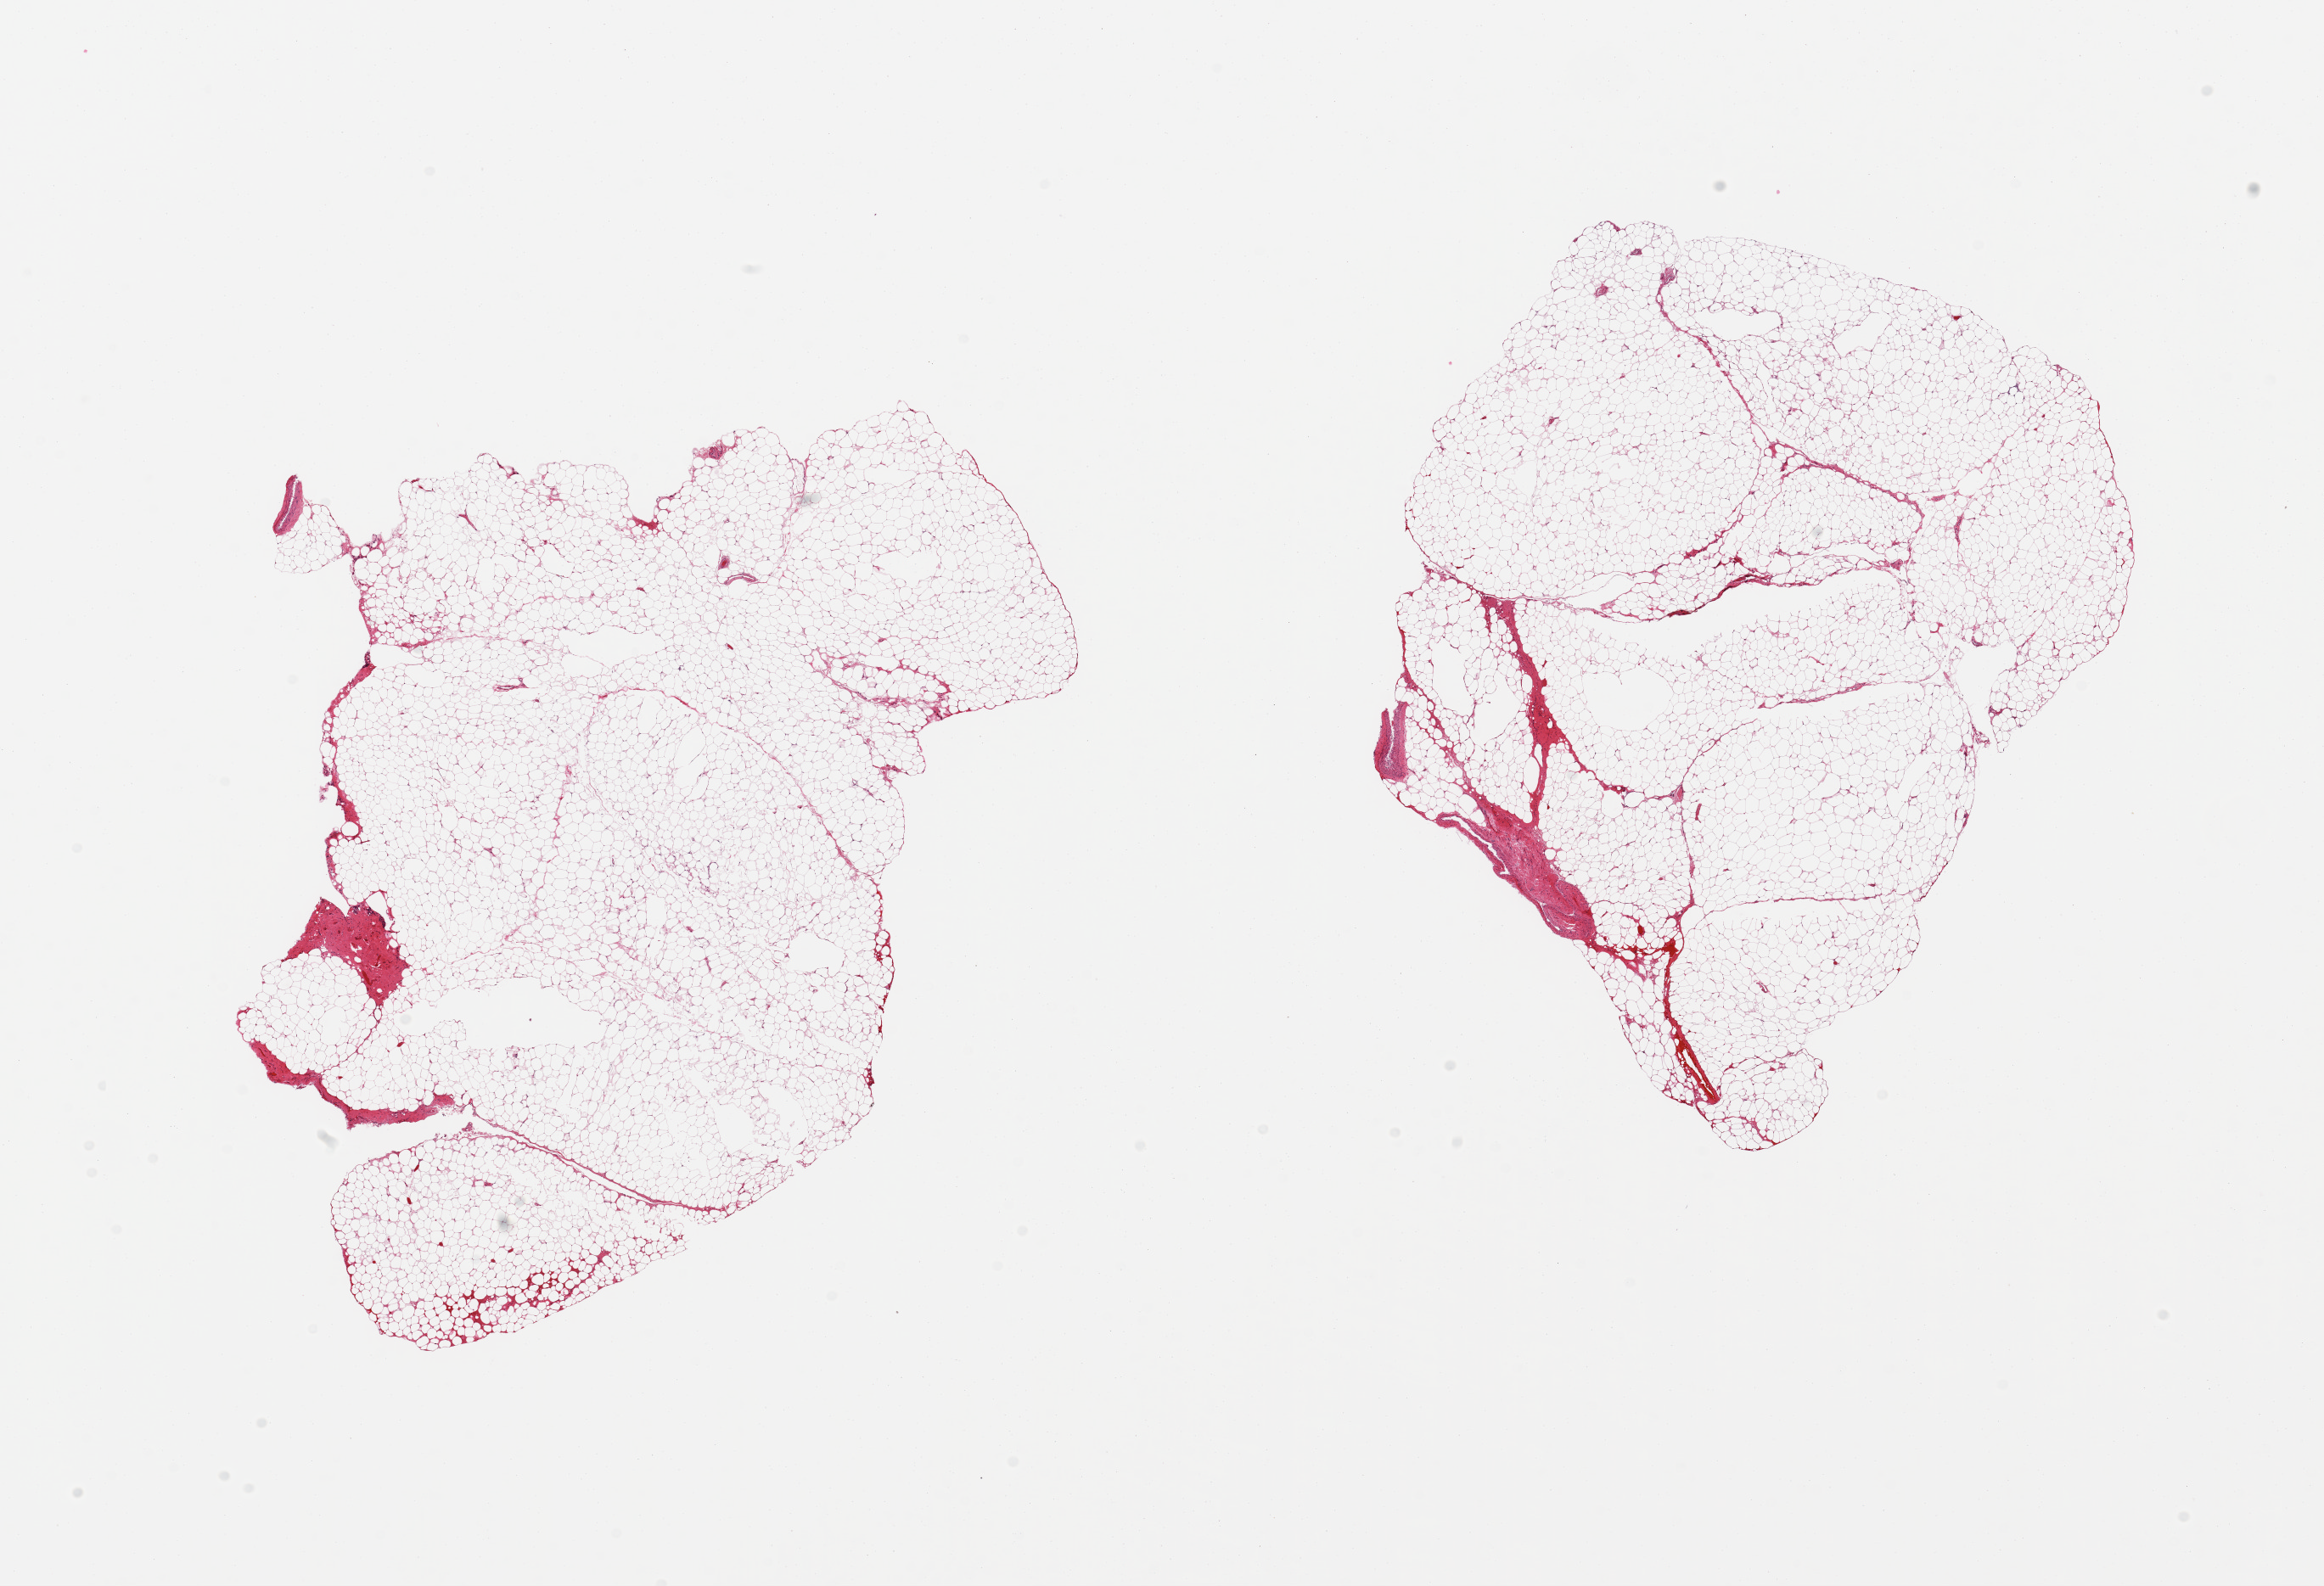
Whole-slide image, H&E stain, brightfield — low-resolution overview of the scanned area, about 21.7 x 14.8 mm (from a 20x scan); PAXgene-fixed, paraffin-embedded tissue; sampled site (target tissue): omentum; tissue donor sample. Male donor.
Review note (as recorded): 2 pieces; <5% fibrous content.